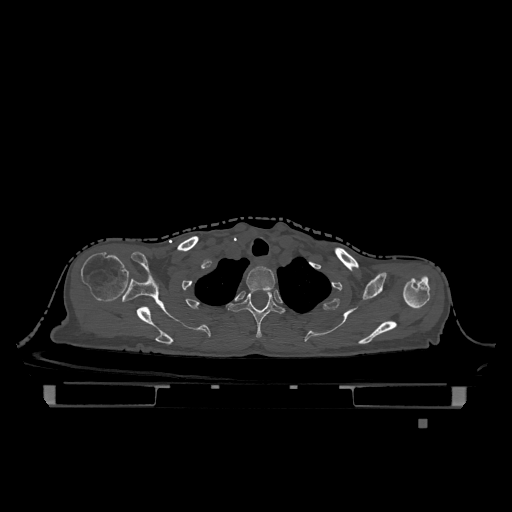
CT including the spine, one axial slice; slice 972 of 1317 in the series (ordered by position); bone window (W 1800 / L 400 HU); 0.5 mm slice thickness; 512 × 512 image matrix, field of view 500 × 500 mm. Patient: female, 74 years. Case-level facts recorded for this patient, not image findings: primary cancer: lung.
Structures marked on this image (semi-automatically segmented with operator editing):
- T1 vertebra: box from (x=246, y=266) to (x=276, y=291) px
- T2 vertebra: (x=228, y=290)–(x=284, y=338)